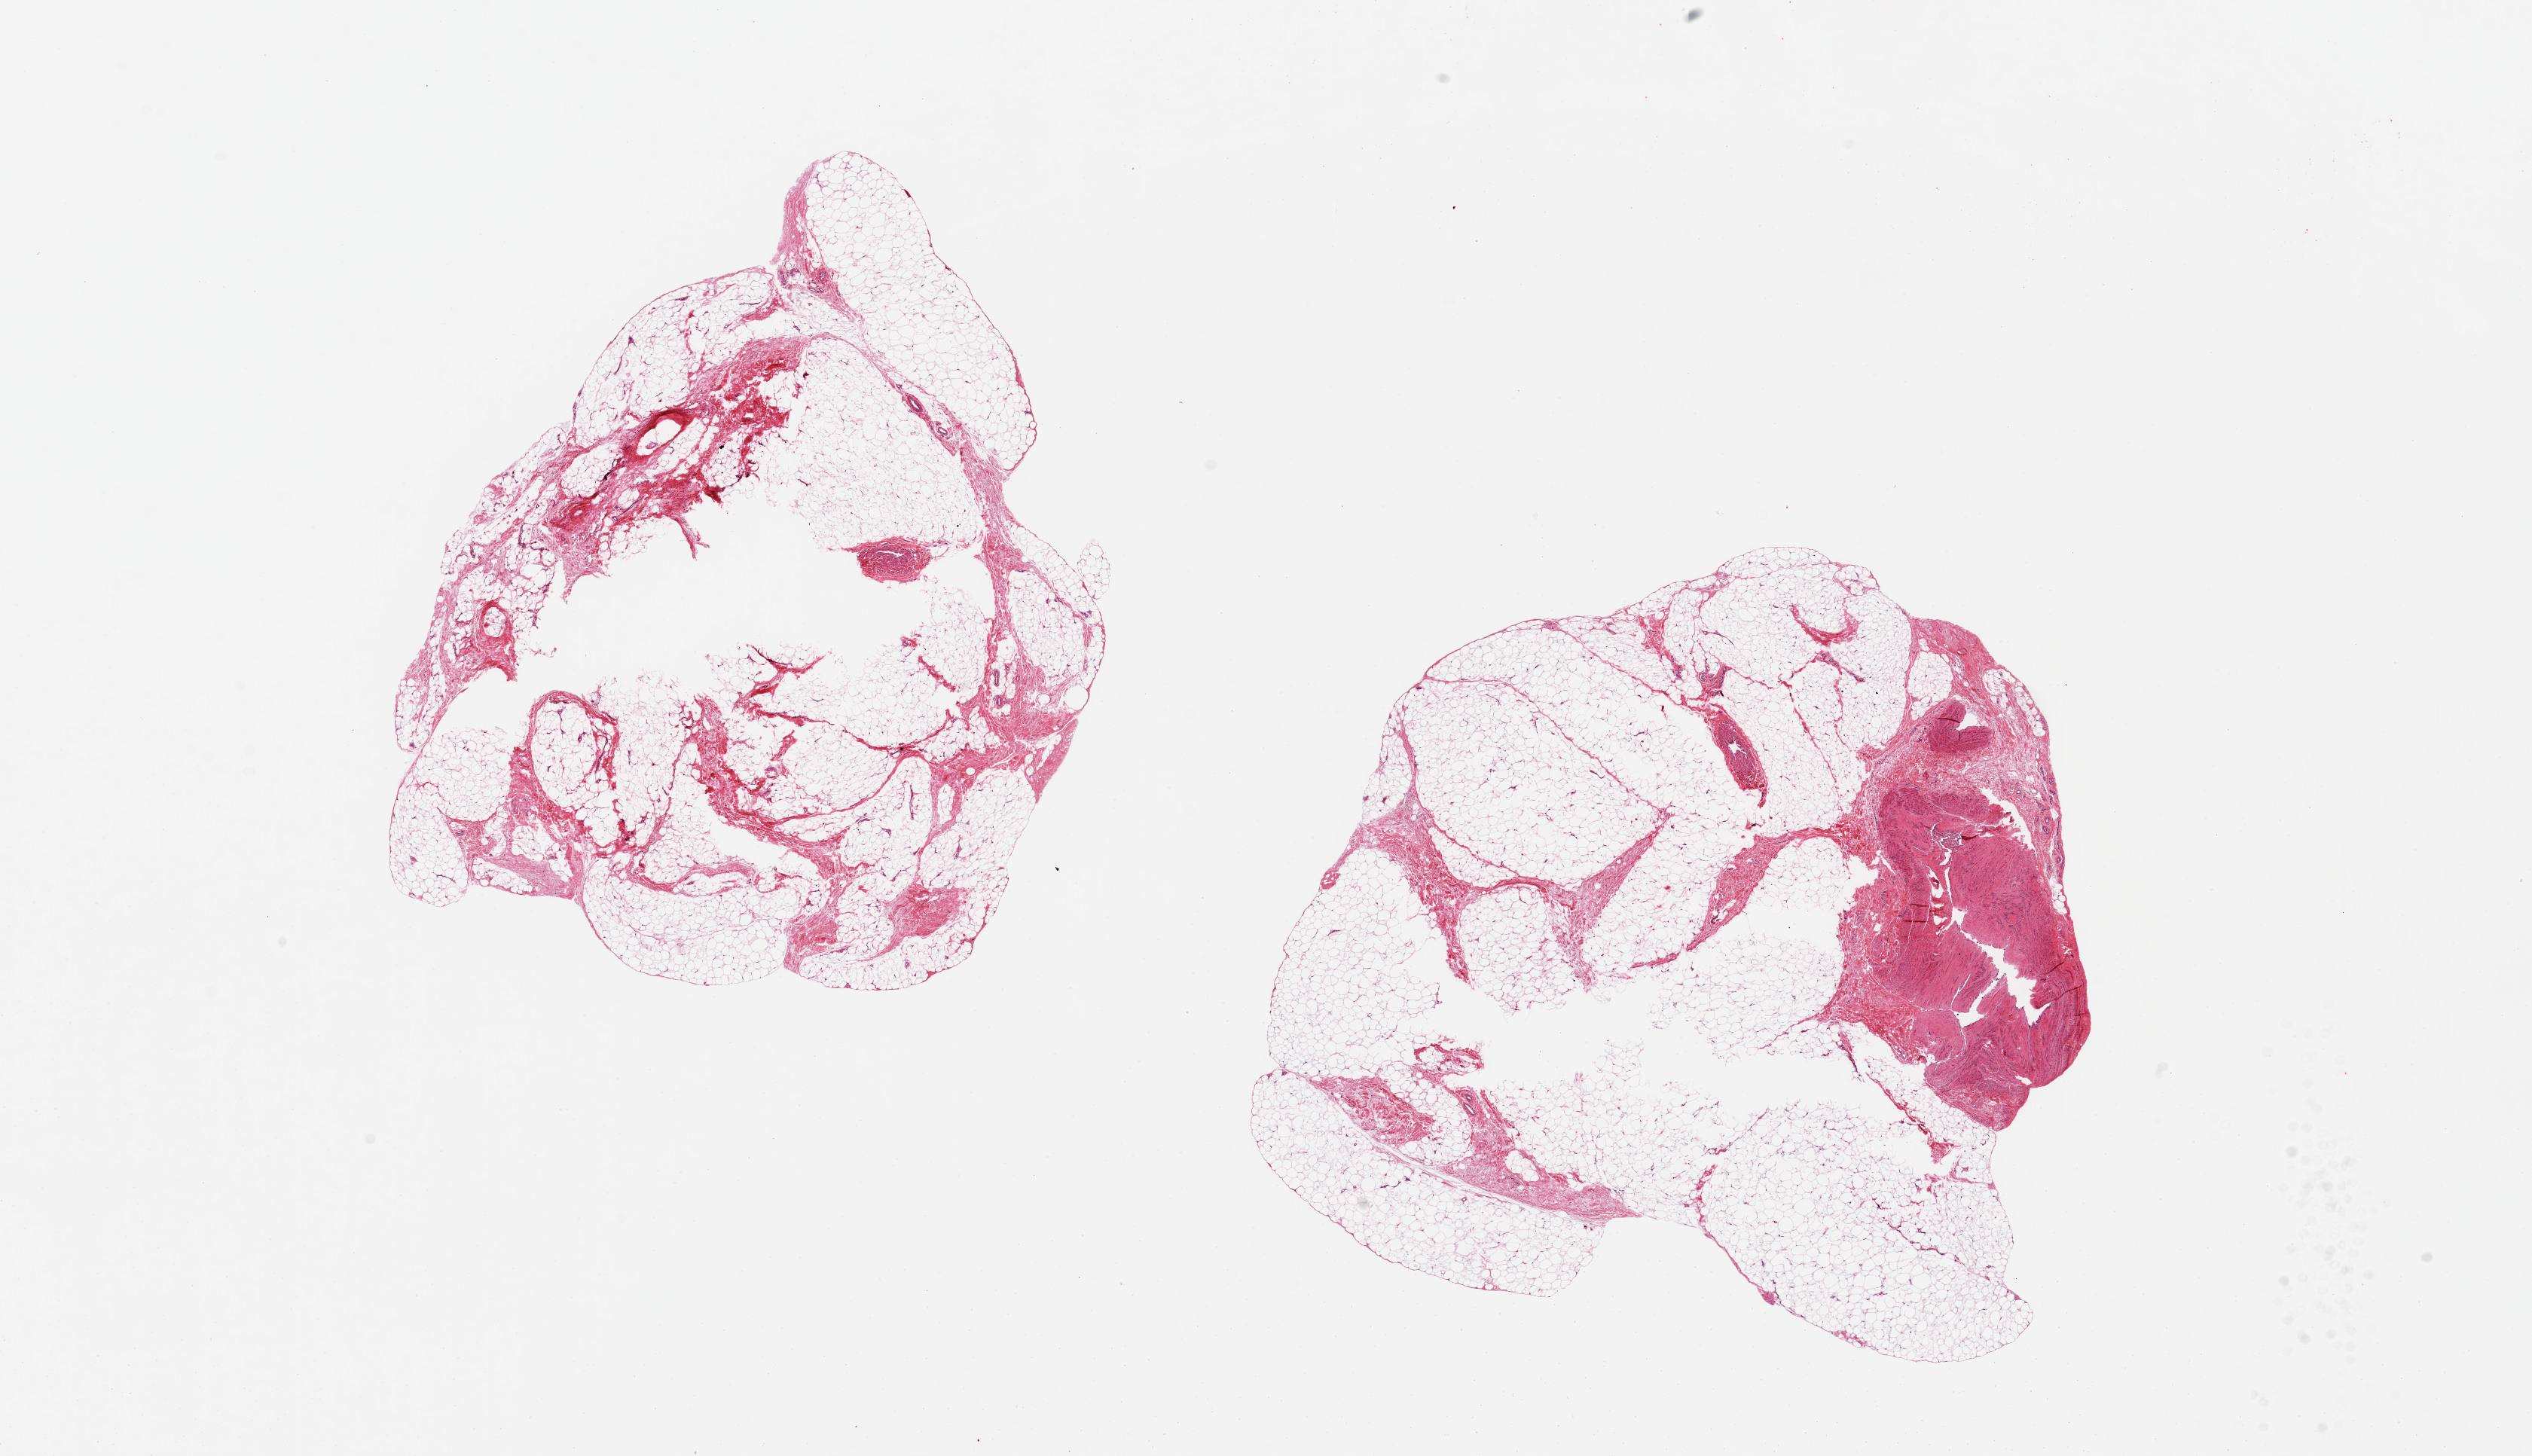
Whole-slide image, haematoxylin and eosin stain, brightfield, a low-resolution overview of the entire scanned area, about 26.6 x 15.3 mm. PAXgene-fixed, paraffin-embedded tissue. Section of adipose tissue (target tissue). Donor tissue sample. Male donor.
Review note (as recorded): 2 pieces, ~8x8mm, fibrous component.